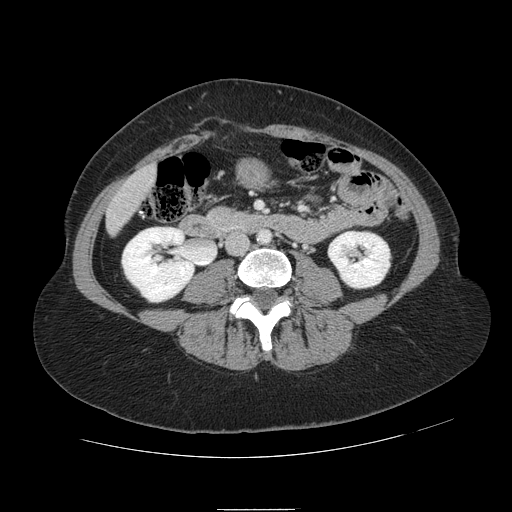
Contrast-enhanced abdominal CT, one axial slice. Slice 8 of 121 in the series (ordered by position). Intravenous contrast given. Soft-tissue window (W 400 / L 40 HU). 2.5 mm slice thickness. 512 × 512 image matrix, field of view 400 × 400 mm. Female patient, age 52 years. Case-level facts recorded for this patient, not image findings: diagnosis: colorectal cancer liver metastases, imaged before liver resection; multiple liver metastases: yes; largest metastasis: 6.3 cm; disease in both lobes: no.
Annotated regions visible in this slice (expert manual segmentation):
- liver: bounding box (x1, y1, x2, y2) in pixels: (107, 167, 156, 233)